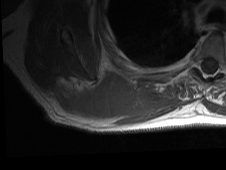
MRI of an extremity soft-tissue mass, one axial slice. Position 23 of 81 along the scan axis. MR volume resampled by the dataset authors to the PET/CT grid (not the native acquisition matrix). 3.27 mm slice thickness. 226 × 170 image matrix, field of view 221 × 166 mm. Male patient. Case-level facts recorded for this patient, not image findings: histological type: pleiomorphic spindle cell undifferentiated; grade: high; site of the primary tumour: right parascapusular.
Outlined on this slice (expert contour drawn on MRI and transferred to this co-registered scan by the dataset authors):
- gross tumour volume including surrounding oedema: bounding box [x1, y1, x2, y2] px = [48, 74, 179, 126]
- gross tumour volume (mass): [64, 77, 136, 119]